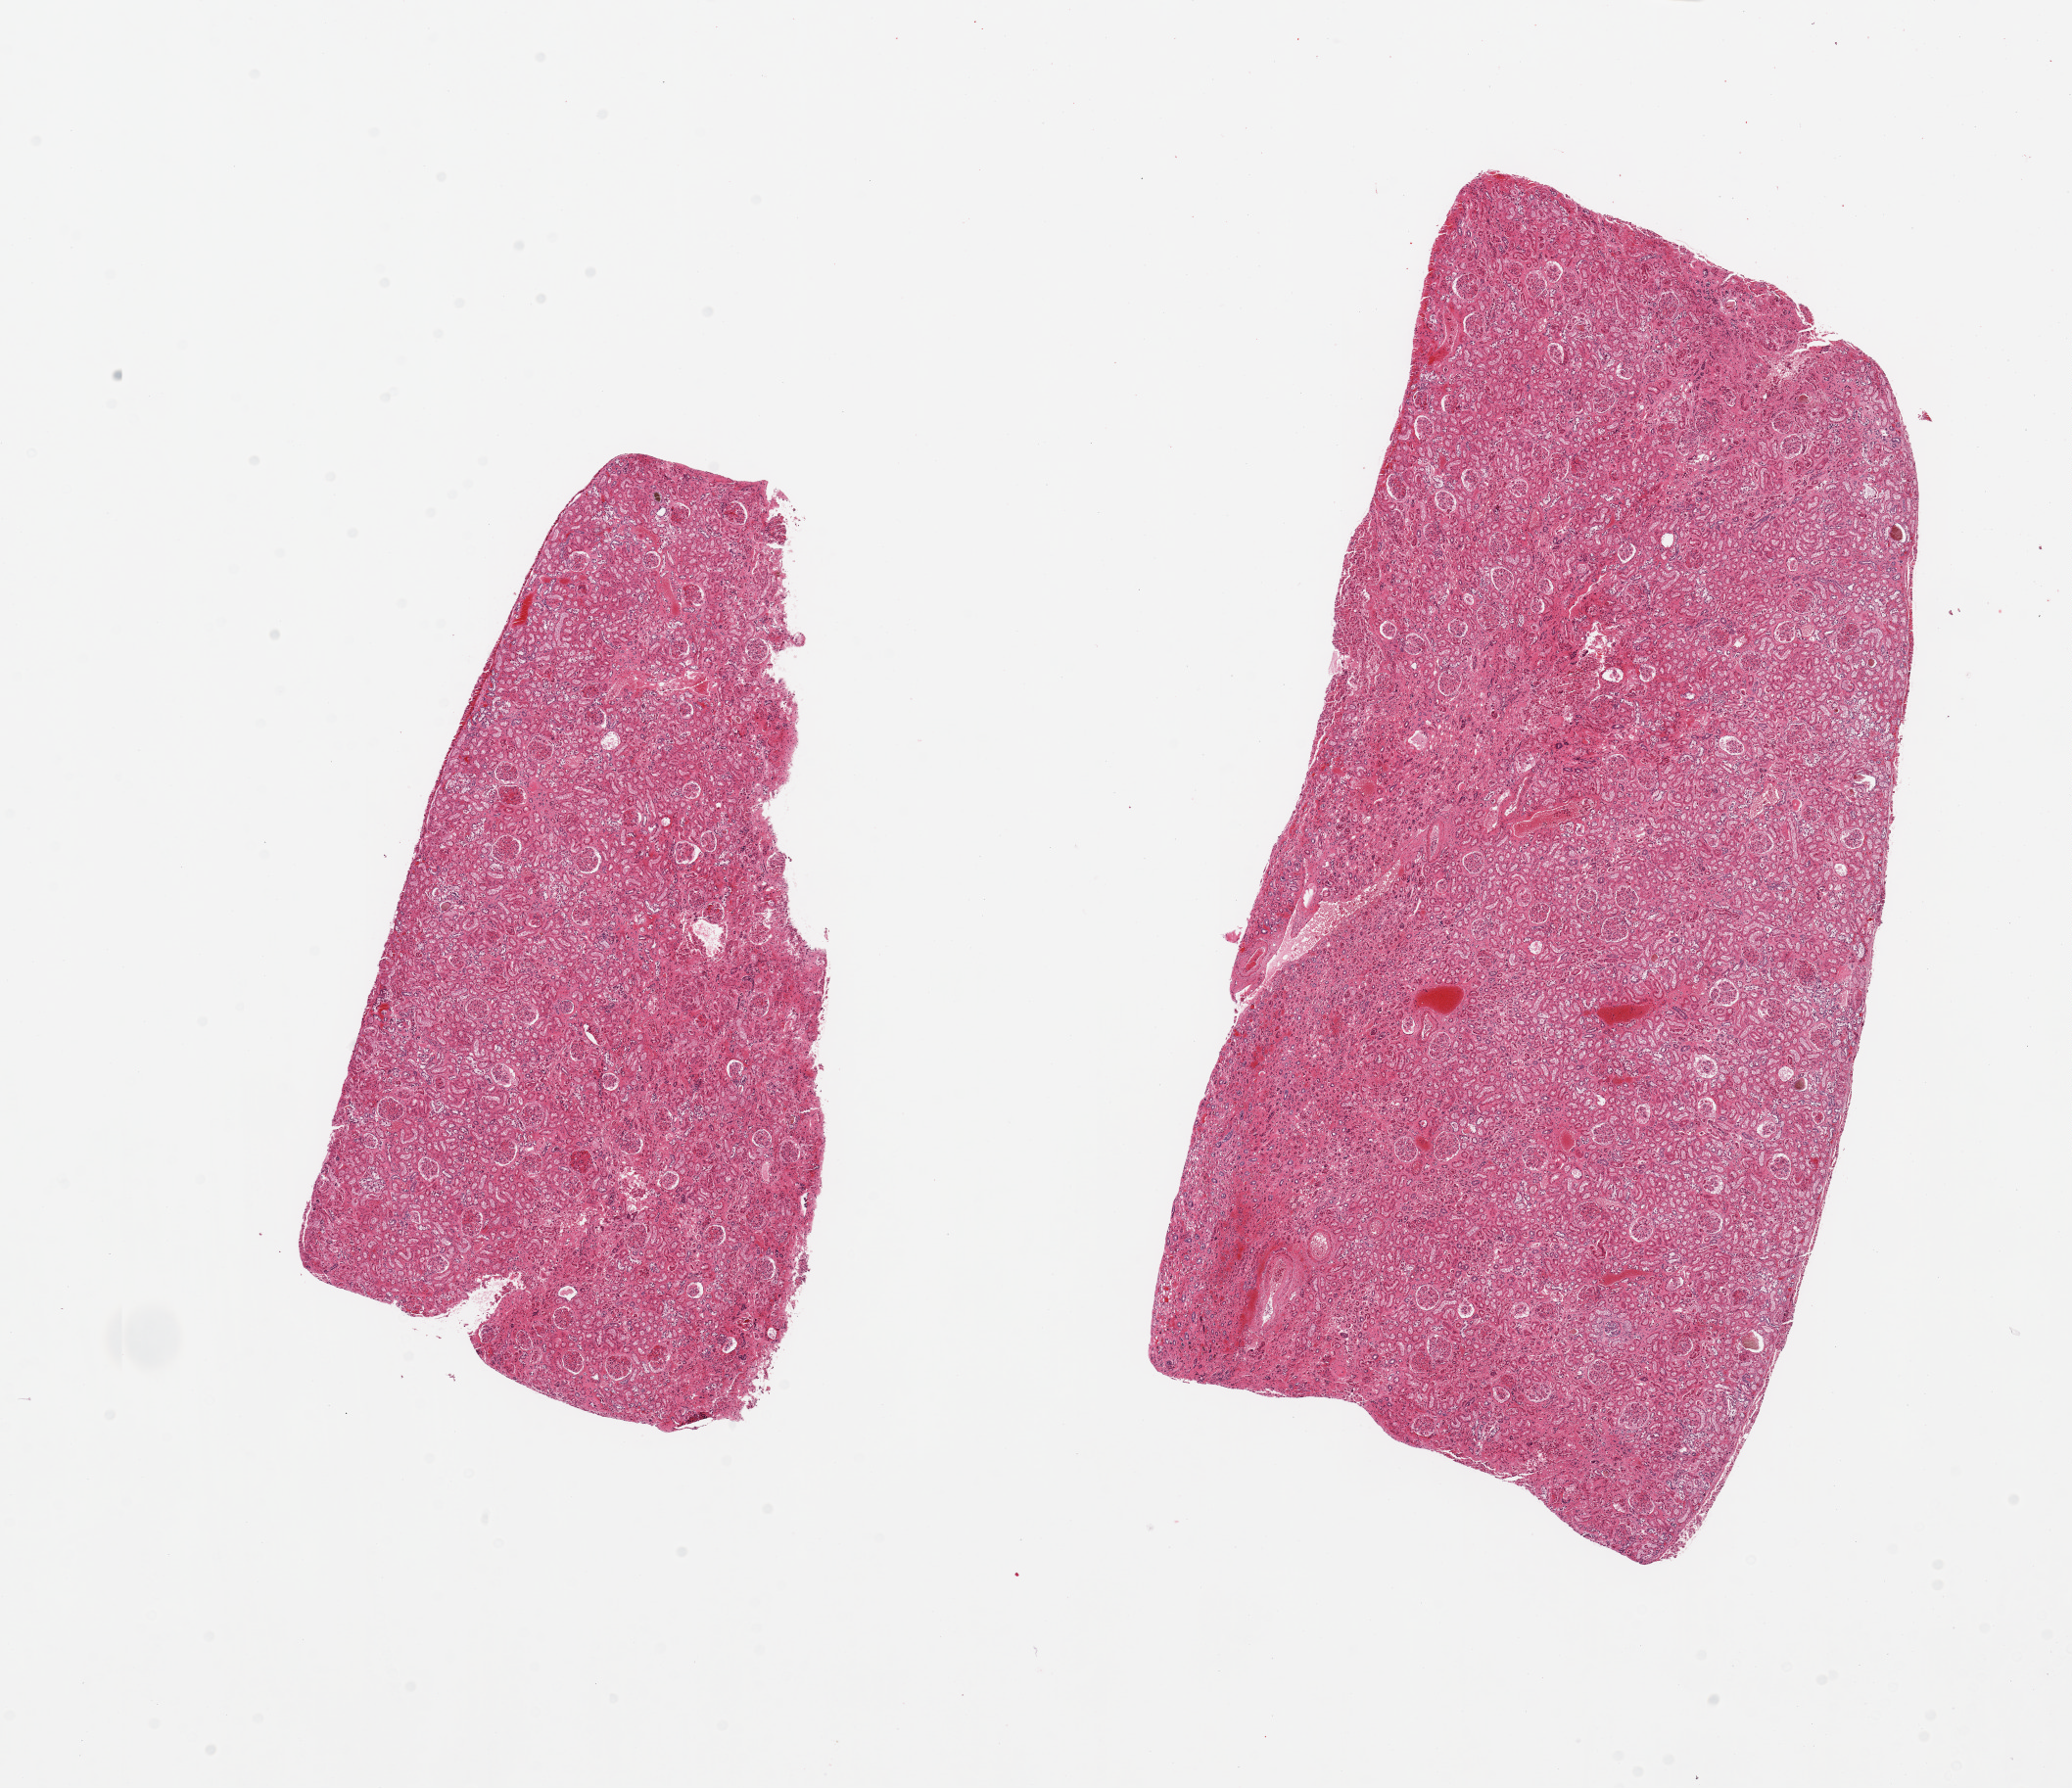
Digitized hematoxylin and eosin (H&E)-stained section, brightfield — shown as a low-resolution overview of the whole scanned area (about 16.7 x 14.4 mm). PAXgene-fixed paraffin-embedded (PFPE) section. Target tissue: renal cortex. Tissue donor sample.
Review note (as recorded): 2 pieces; no active or chronic lesions.